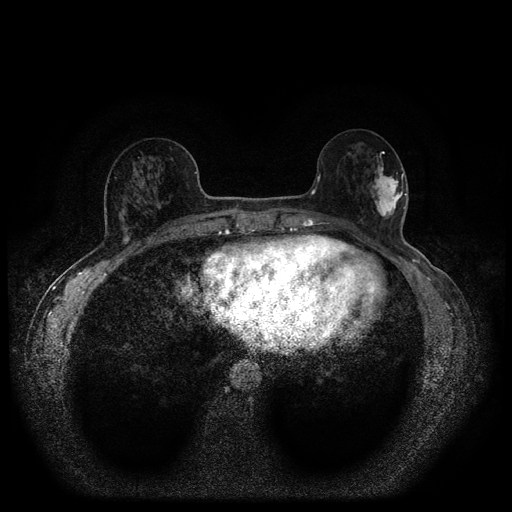
Breast MRI (dynamic contrast-enhanced, multi-phase), one axial slice. Slice 41 of 116 in the series (ordered by position). Dynamic contrast-enhanced series, time point 2 of 5 at this slice position (early post-contrast). 1.5 T. TE 2.7 ms, TR 5.4 ms. 2 mm slice thickness. 512 × 512 image matrix, field of view 330 × 330 mm. Patient: female, 56 years.
Outlined on this slice (semi-automatic segmentation, software-assisted and operator-edited):
- breast lesion (labelled 'tumour' in the annotation; benign lesions carry a separate 'benign' label): bounding box [x1, y1, x2, y2] px = [368, 151, 405, 225]